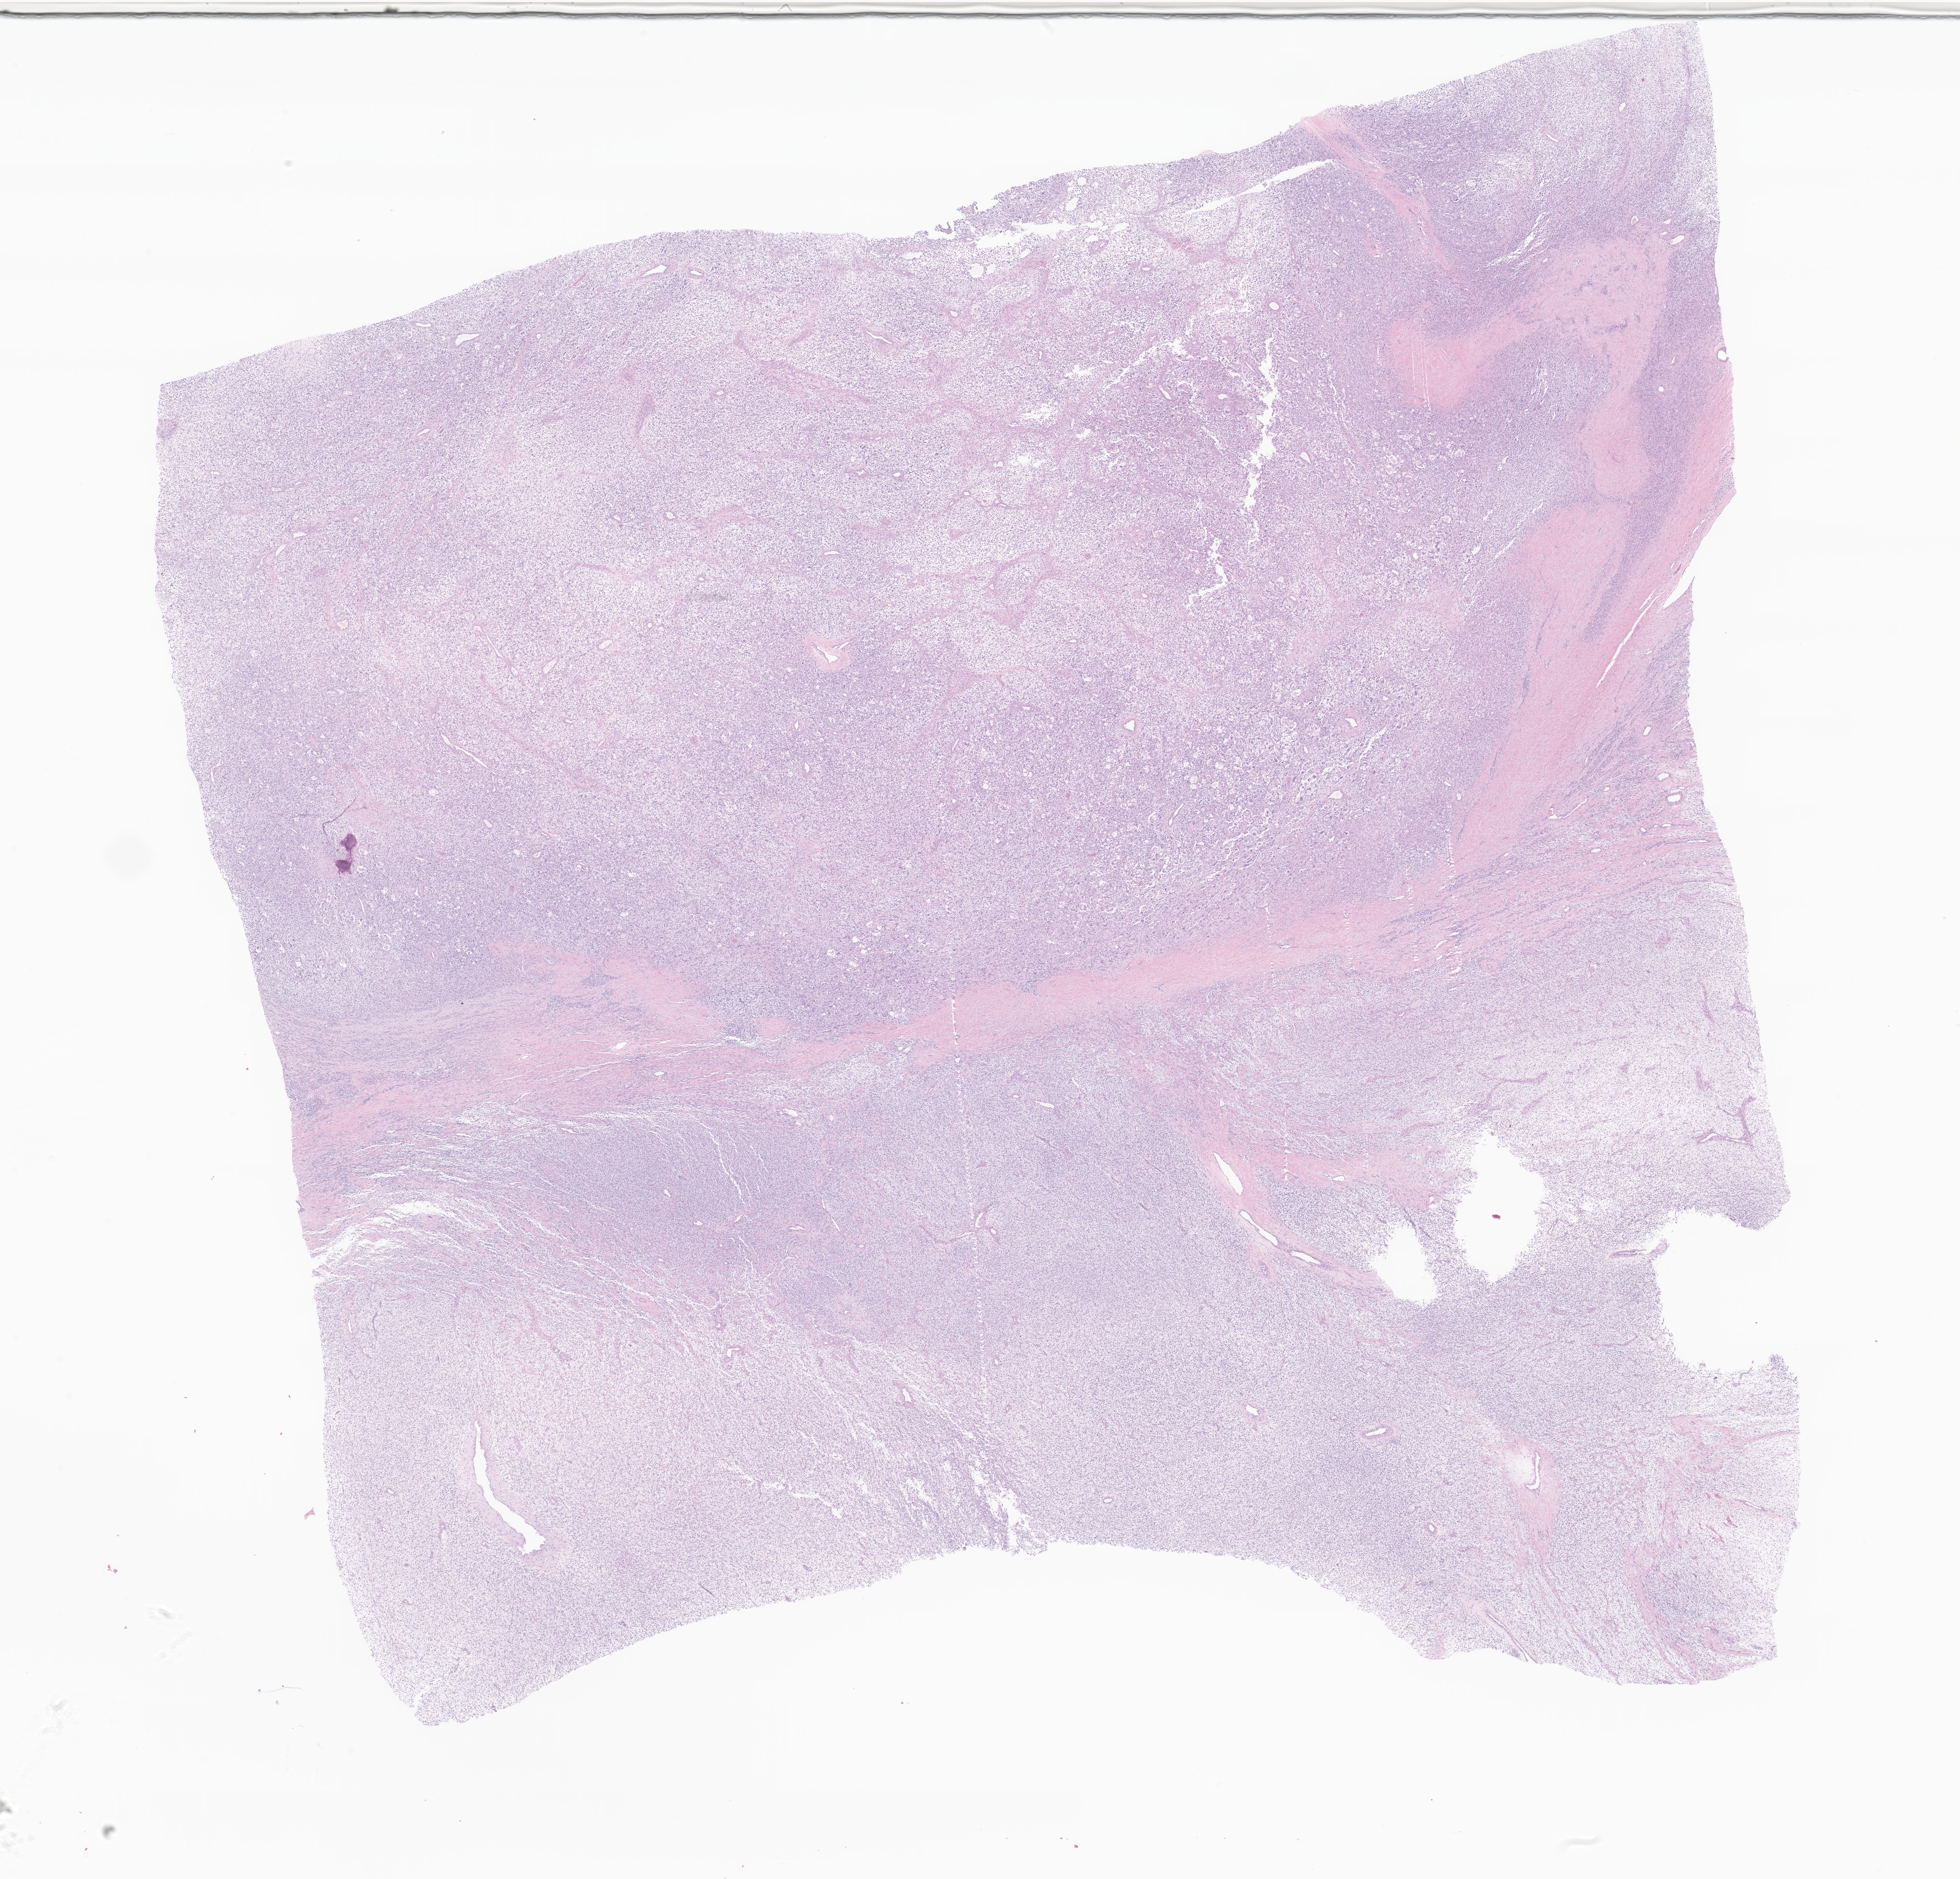
Whole-slide image, hematoxylin and eosin (H&E) stain of tumor tissue from the male genital organ, whole scanned area (about 23.3 x 22.4 mm) shown as a low-resolution overview. Formalin-fixed, paraffin-embedded (FFPE) tissue. Male patient, age 86 months (7 years 2 months).
Diagnosis: Rhabdomyosarcoma, NOS.